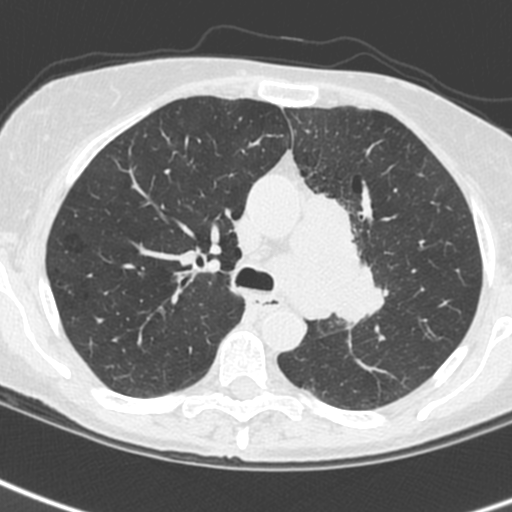
Low-dose screening chest CT, one axial slice; position 165 of 242 along the scan axis; 120 kVp; lung window (W 1500 / L -600 HU); 1.3 mm slice thickness; 512 × 512 image matrix, field of view 284 × 284 mm.
Structures marked on this image (expert manual segmentation):
- lesion 3 (tumor, upper lobe of left lung): bounding box [x1, y1, x2, y2] px = [310, 193, 386, 325]